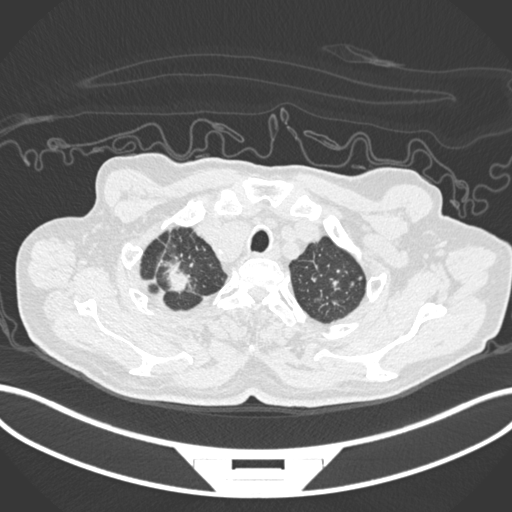
Chest CT, one axial slice. Position 198 of 207 along the scan axis. Reconstruction kernel B30f. 120 kVp. Lung window (W 1500 / L -600 HU). 1 mm slice thickness. 512 × 512 image matrix, field of view 400 × 400 mm. Male patient, age 69 years. Case-level facts recorded for this patient, not image findings: clinical TNM (as recorded): T1c N1 M1.
Structures marked on this image (bounding box drawn by a radiologist):
- lung tumour (recorded histology: adenocarcinoma): bounding box (x1, y1, x2, y2) in pixels: (160, 258, 194, 300)